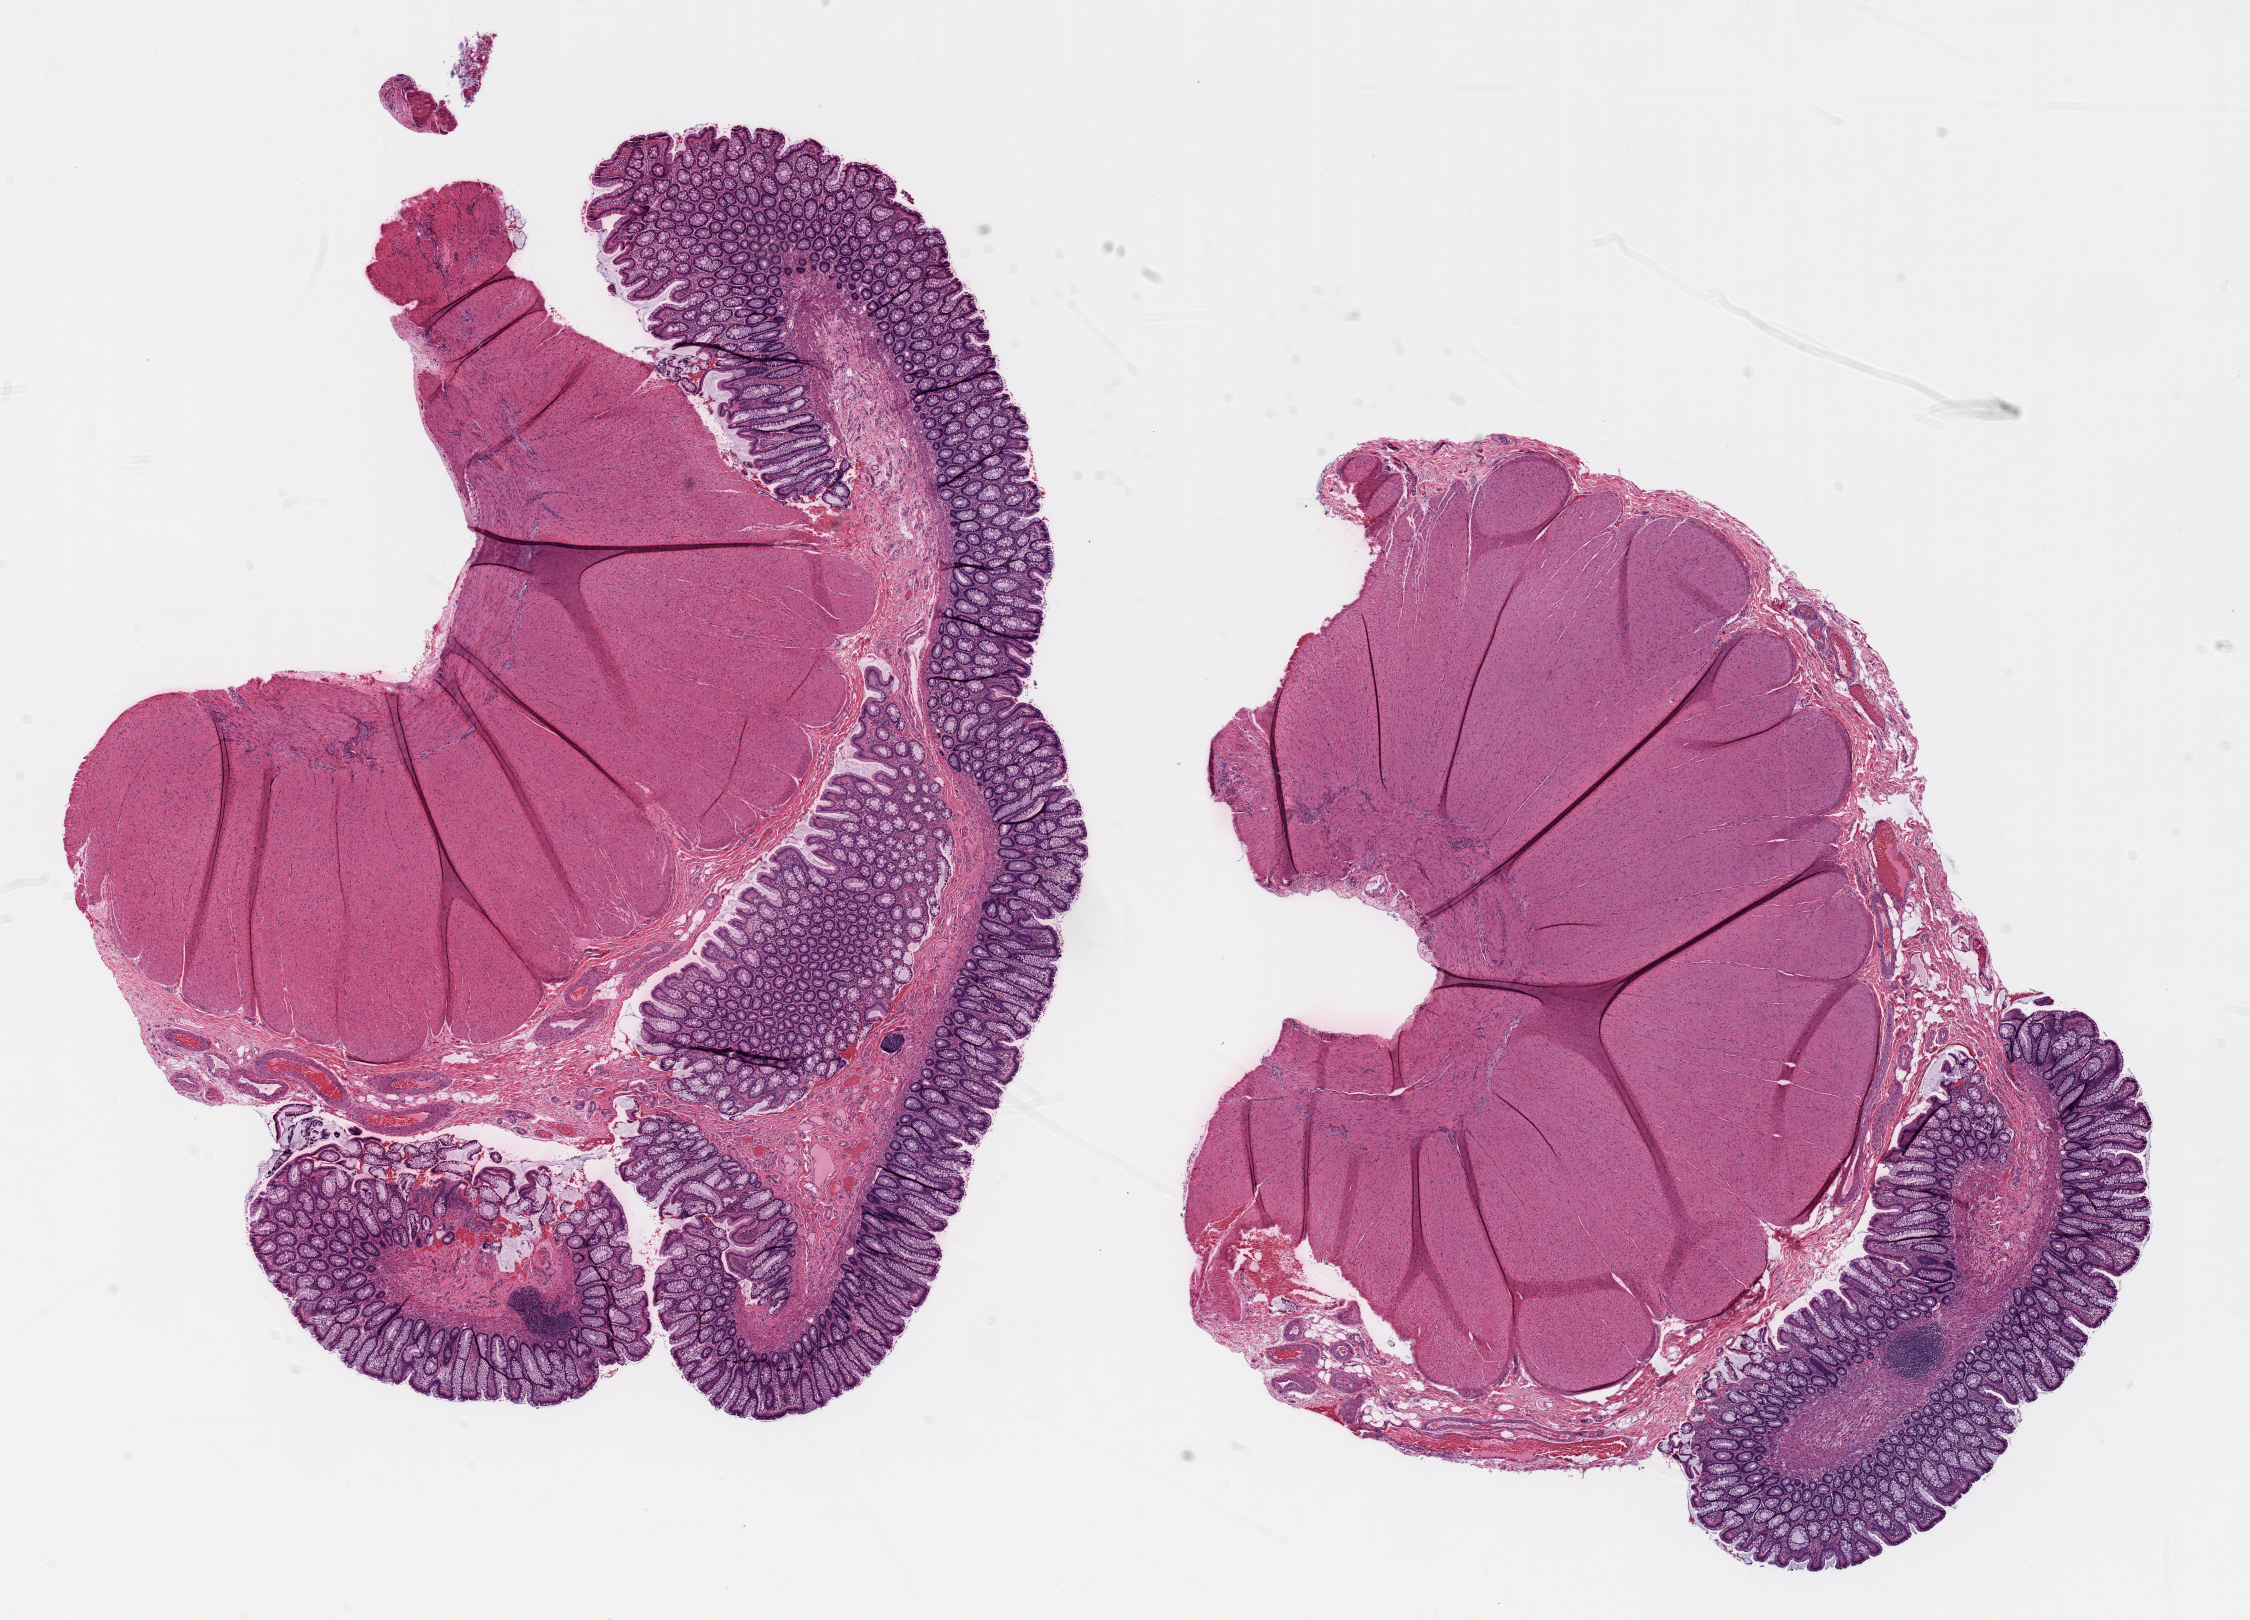
H&E-stained whole-slide image — a low-resolution overview of the entire scanned area, about 18.1 x 13.0 mm (from a 20x scan). Frozen section. Solid tissue normal (non-tumour tissue) sample from the colon. Patient: female, age at initial diagnosis 53 years.
This section: solid tissue normal (non-tumour) sample from the same patient. Patient diagnosis: Adenocarcinoma, NOS.